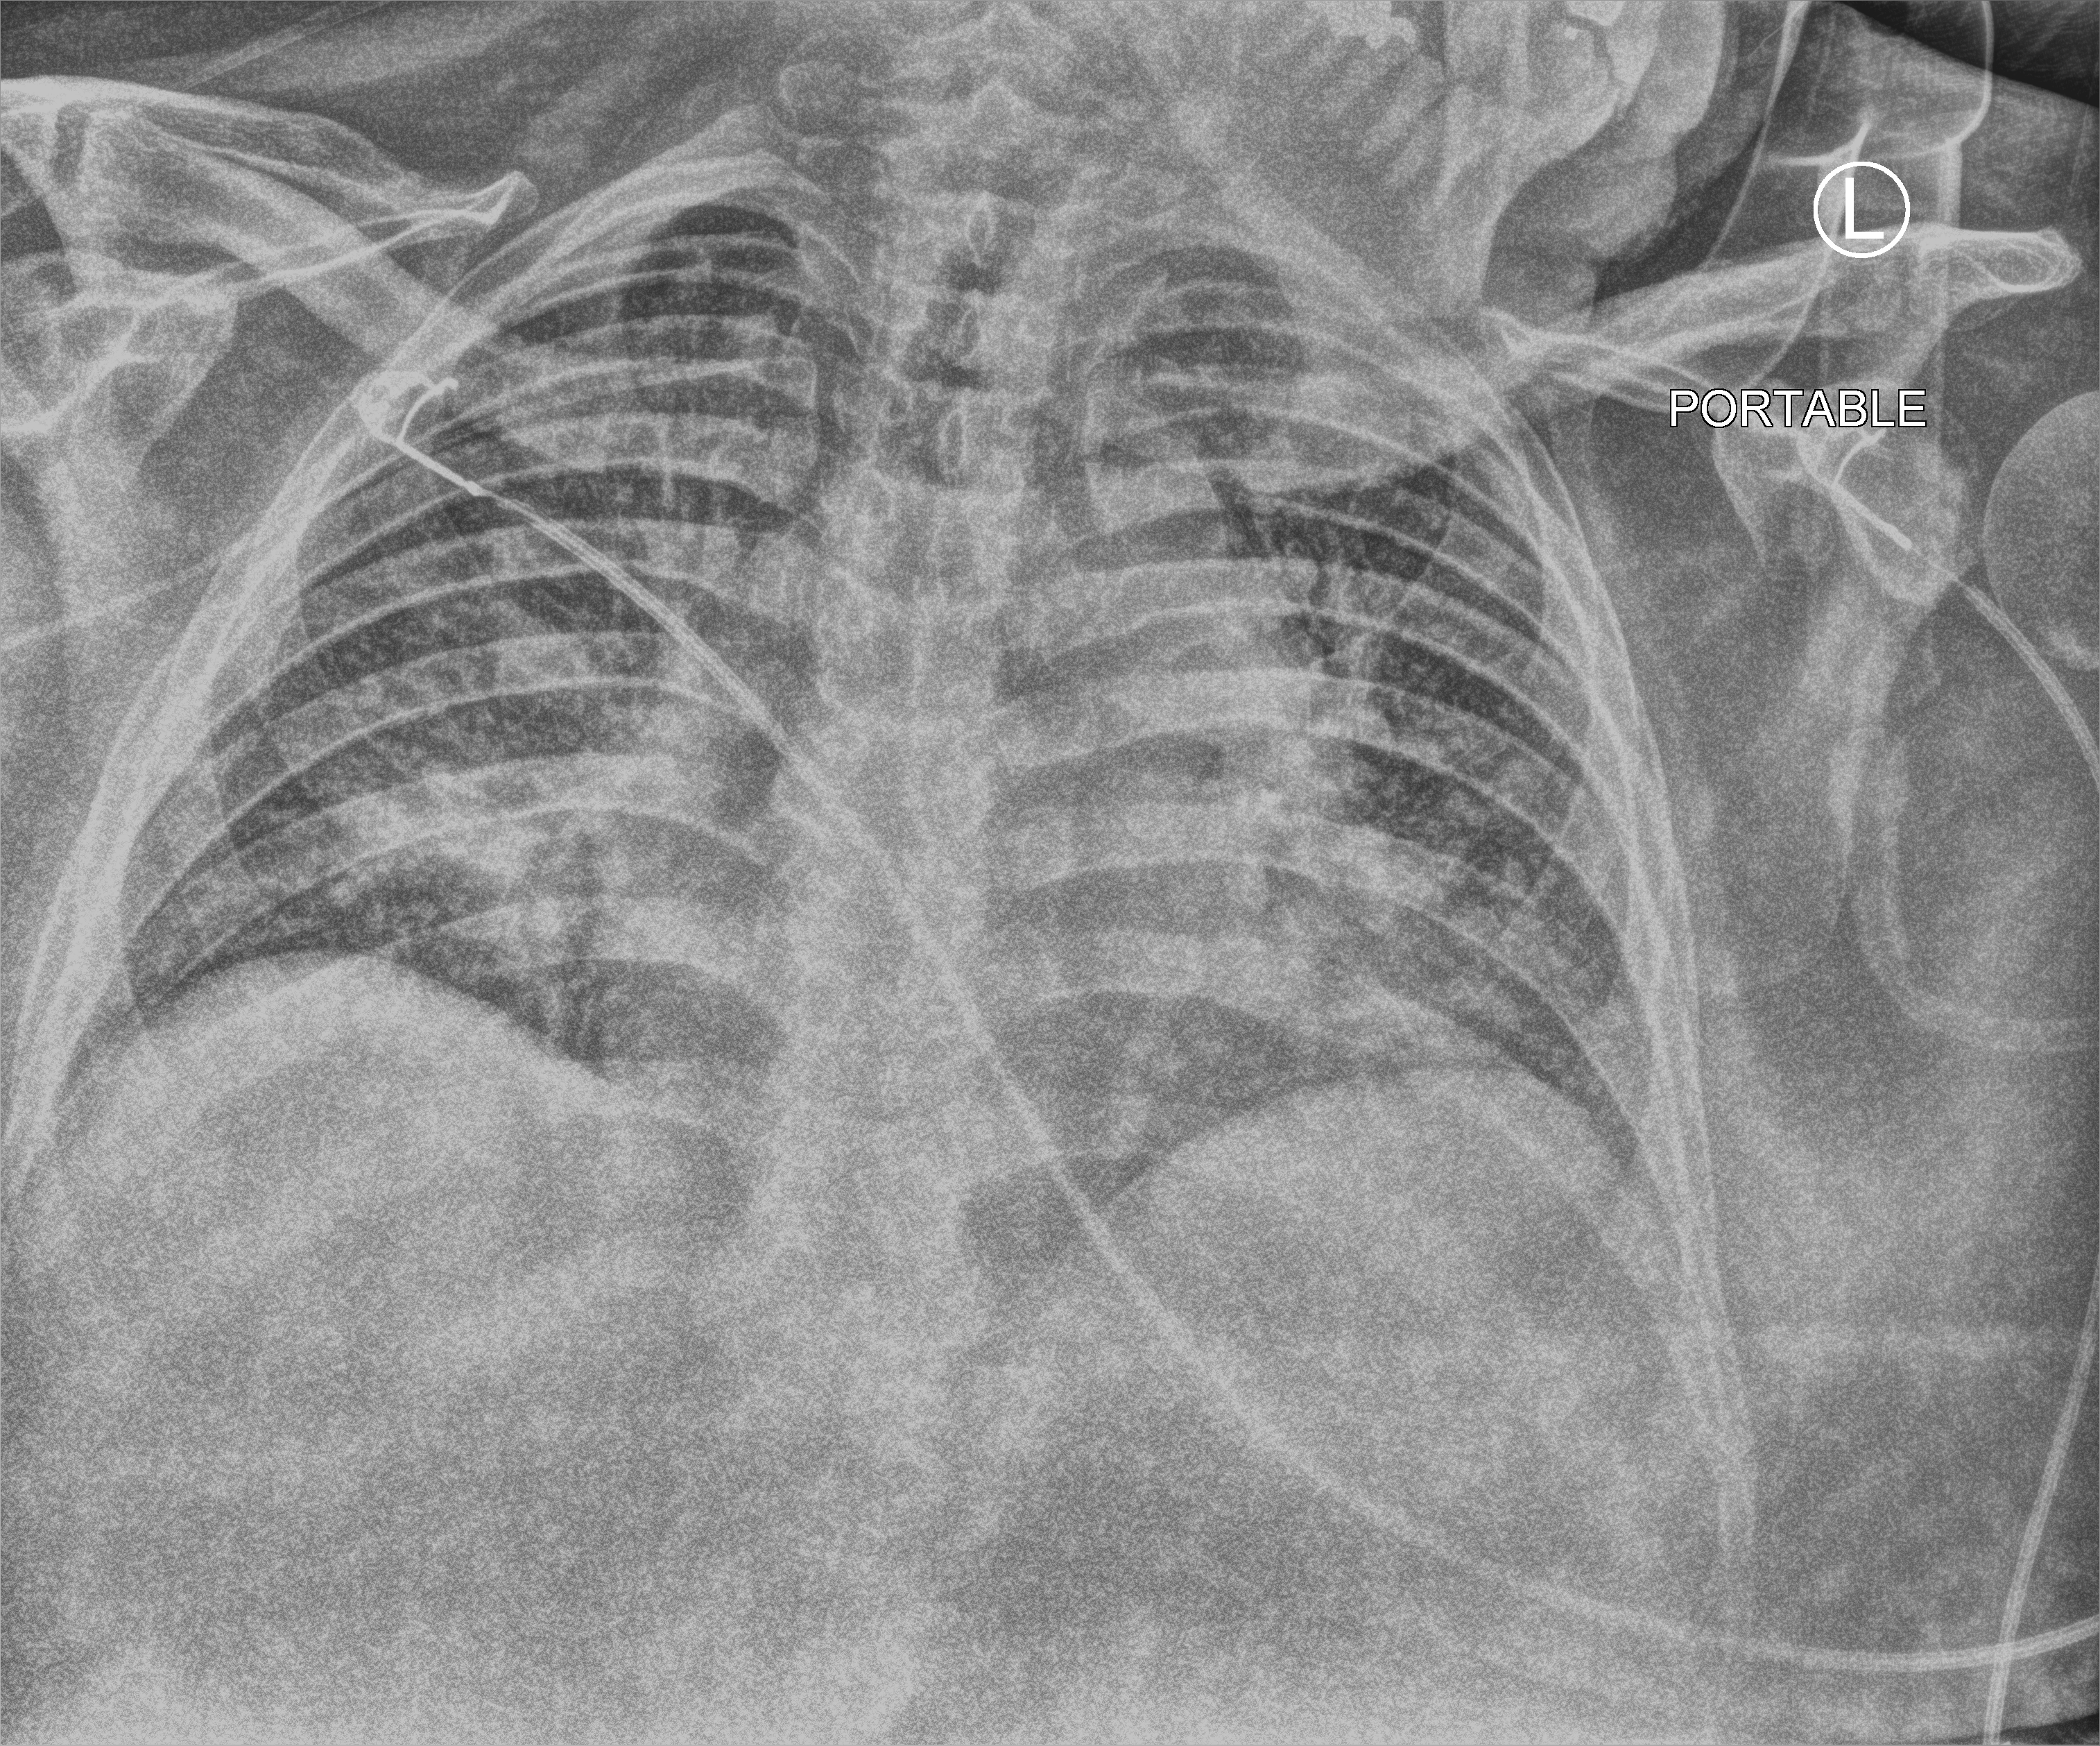
Portable chest radiograph; anteroposterior (AP) projection. Patient hospitalised with COVID-19; male, aged 18–59 years.
Hospital-stay facts (about this admission, not read from this image; timing relative to this image not recorded):
- admitted to intensive care during this hospital stay: yes
- mechanically ventilated during this hospital stay: yes